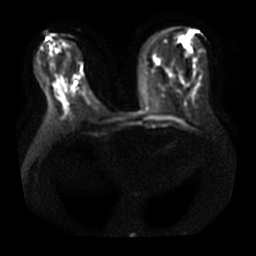
Breast MRI, one axial slice; position 15 of 38 along the scan axis; diffusion-weighted series; image 2 of 4 stored at this slice position (different b-values; order by instance number); 3 T; 5 mm slice thickness; 256 × 256 image matrix, field of view 360 × 360 mm. Female patient.
Structures marked on this image (outlined manually by an expert reader):
- tumour on diffusion-weighted imaging: bounding box (x1, y1, x2, y2) in pixels: (77, 76, 80, 79)